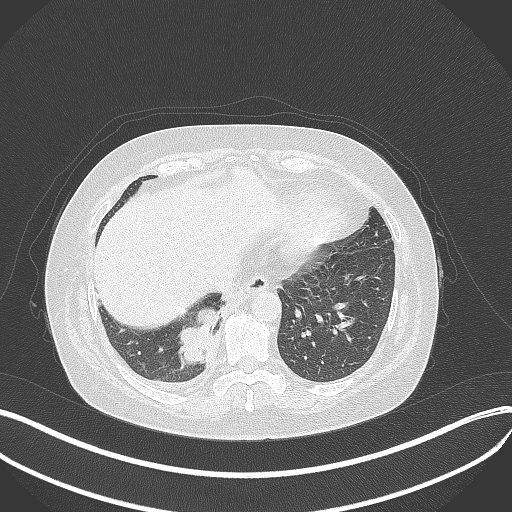
Chest CT, one axial slice. Position 97 of 381 along the scan axis. Lung window (W 1500 / L -600 HU). 1 mm slice thickness. 512 × 512 image matrix, field of view 400 × 400 mm. Patient: female, 56 years. Case-level facts recorded for this patient, not image findings: clinical TNM (as recorded): T2b N1 M0; histopathological grade: G3.
Structures marked on this image (bounding box drawn by a radiologist):
- lung tumour (recorded histology: small cell carcinoma): box from (x=174, y=303) to (x=223, y=375) px